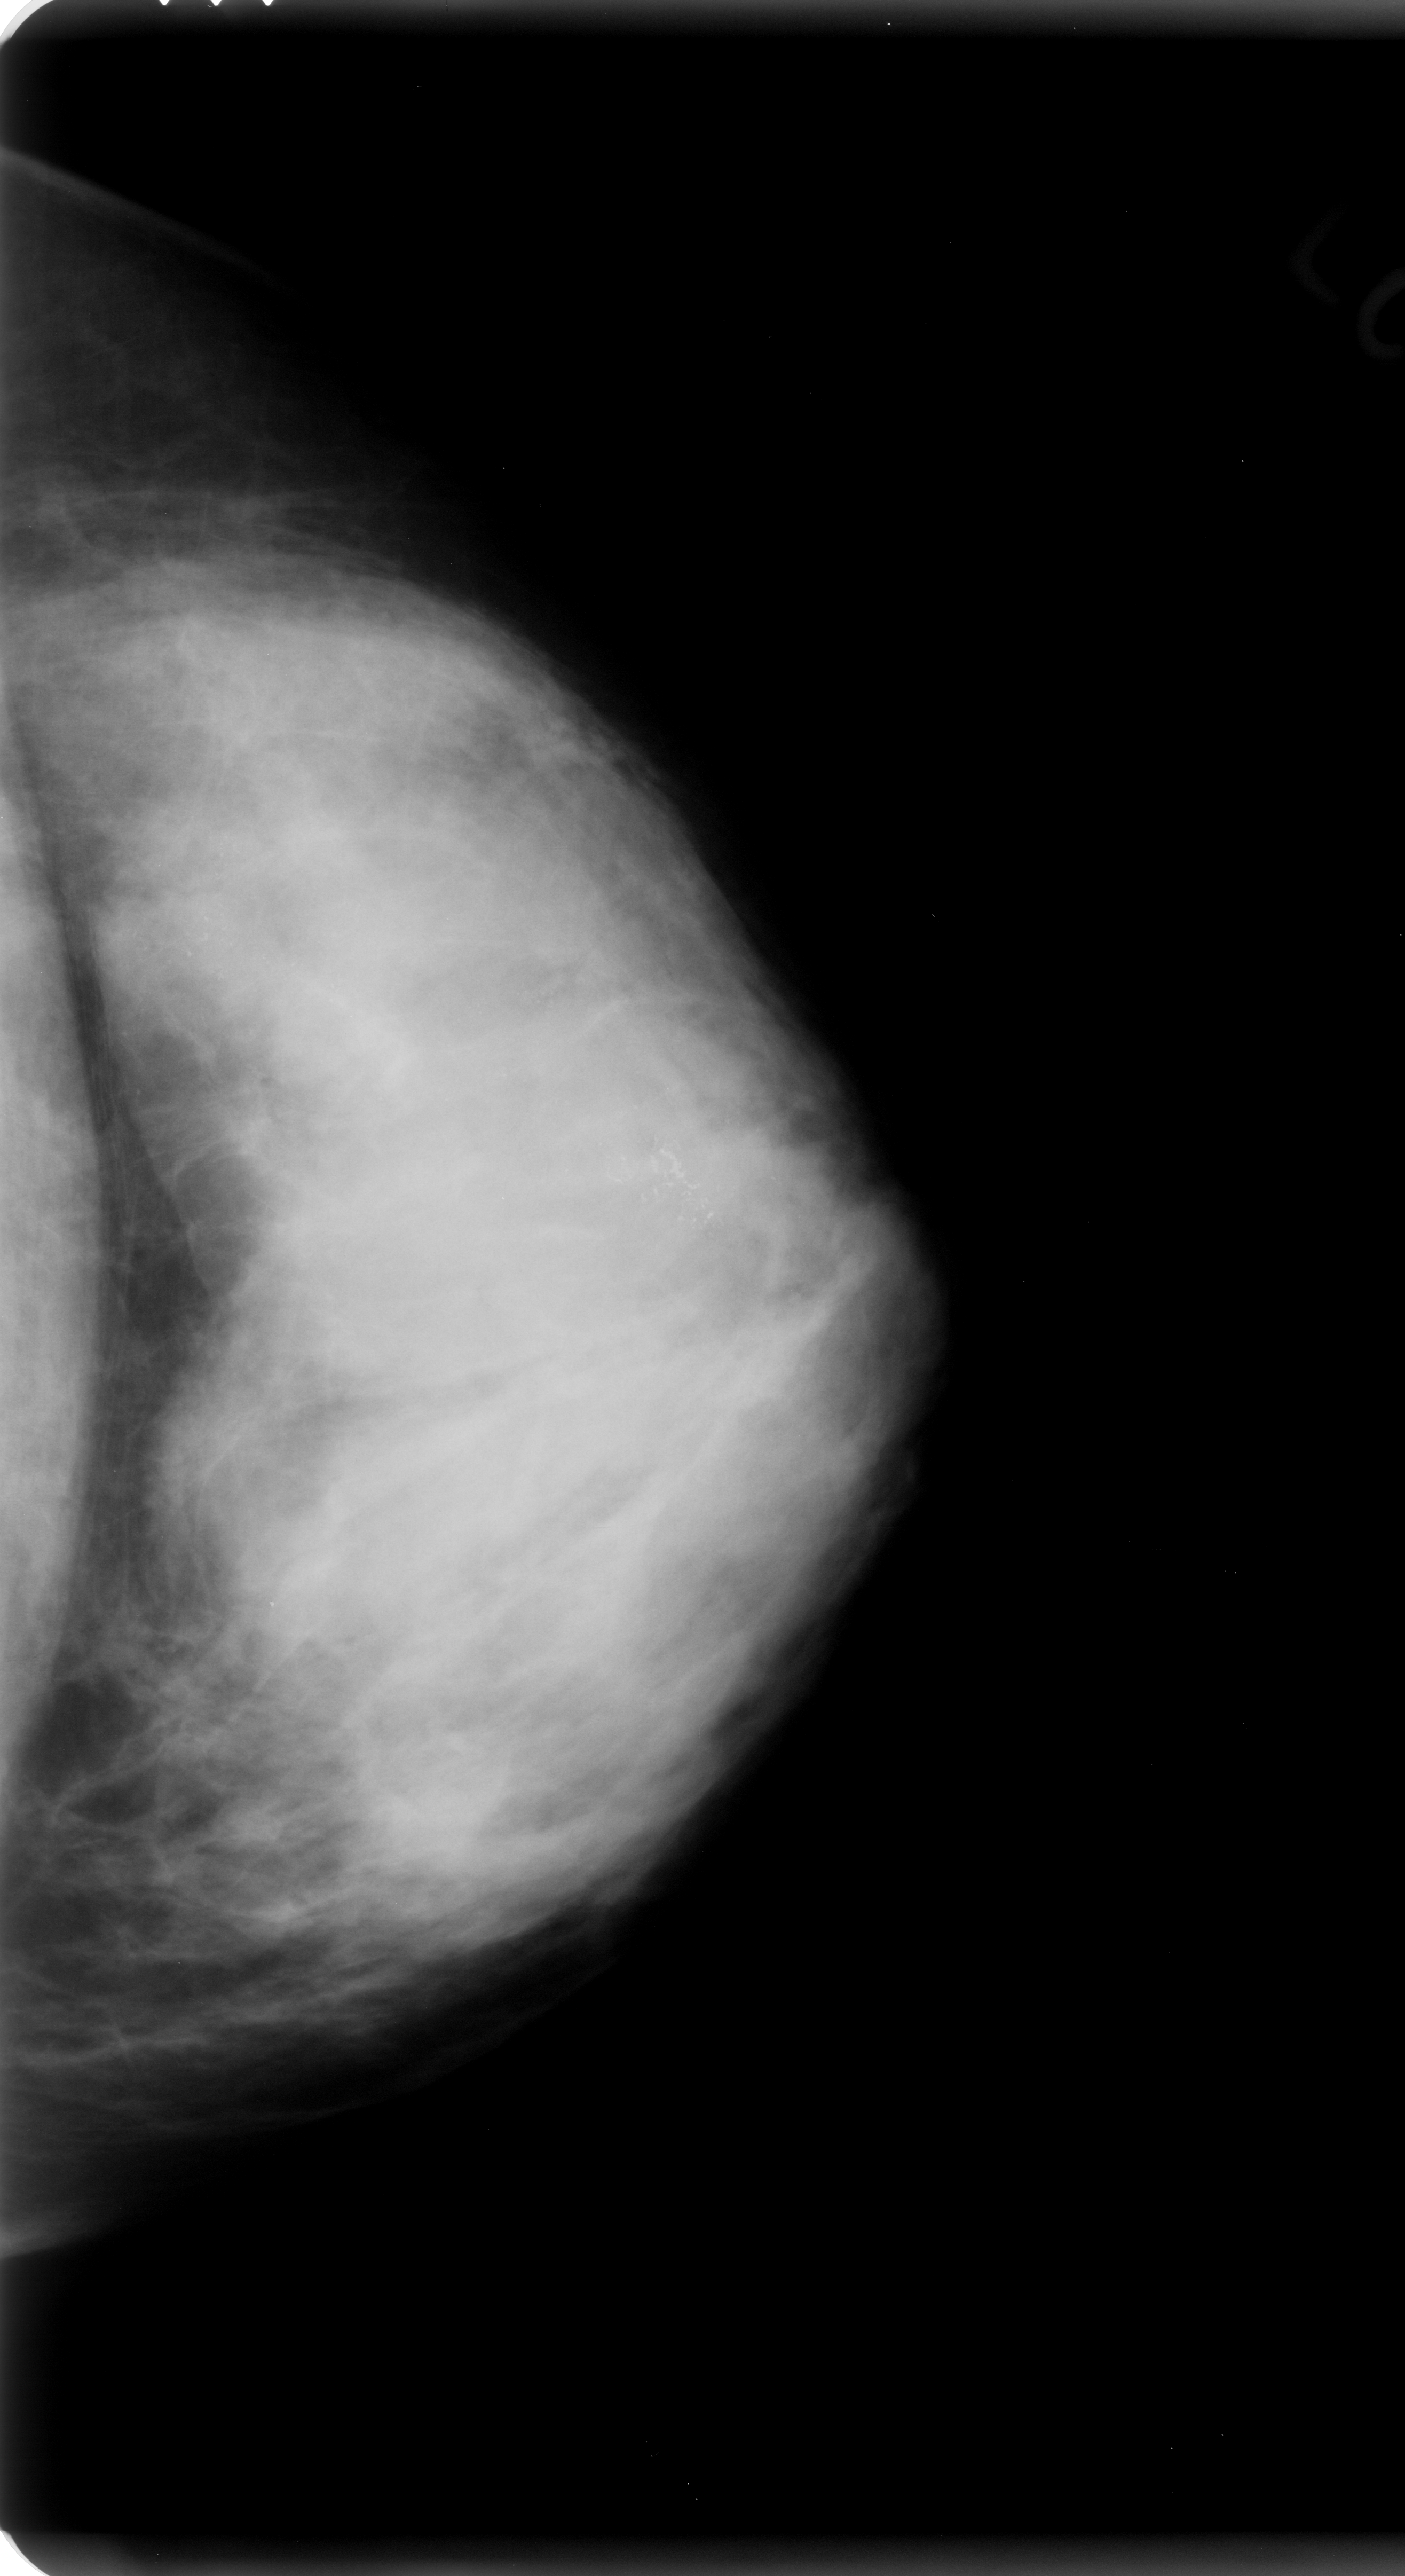
Digitized screen-film mammogram. Left breast. Craniocaudal (CC) view. BI-RADS breast density category 4 (scale 1–4). 1405 × 2576 image matrix.
Marked abnormalities (boxes around the expert regions of interest):
- calcifications, morphology amorphous / pleomorphic, distribution segmental; BI-RADS assessment category 5; subtlety rating 5 on a 1 (subtle) to 5 (obvious) scale; pathology (as recorded): malignant: box from (x=51, y=640) to (x=872, y=1360) px